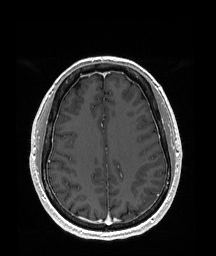
Brain MRI from a brain-tumour surgery series, one axial slice; slice 70 of 192 in the series (ordered by position); T1-weighted post-contrast; 1 mm slice thickness; 216 × 256 image matrix. From the clinical record (not read from this slice): histopathology: Glioblastoma; WHO grade: 4; IDH mutation: no.
Structures marked on this image (expert manual segmentation):
- tumour: bounding box (x1, y1, x2, y2) in pixels: (144, 187, 157, 203)